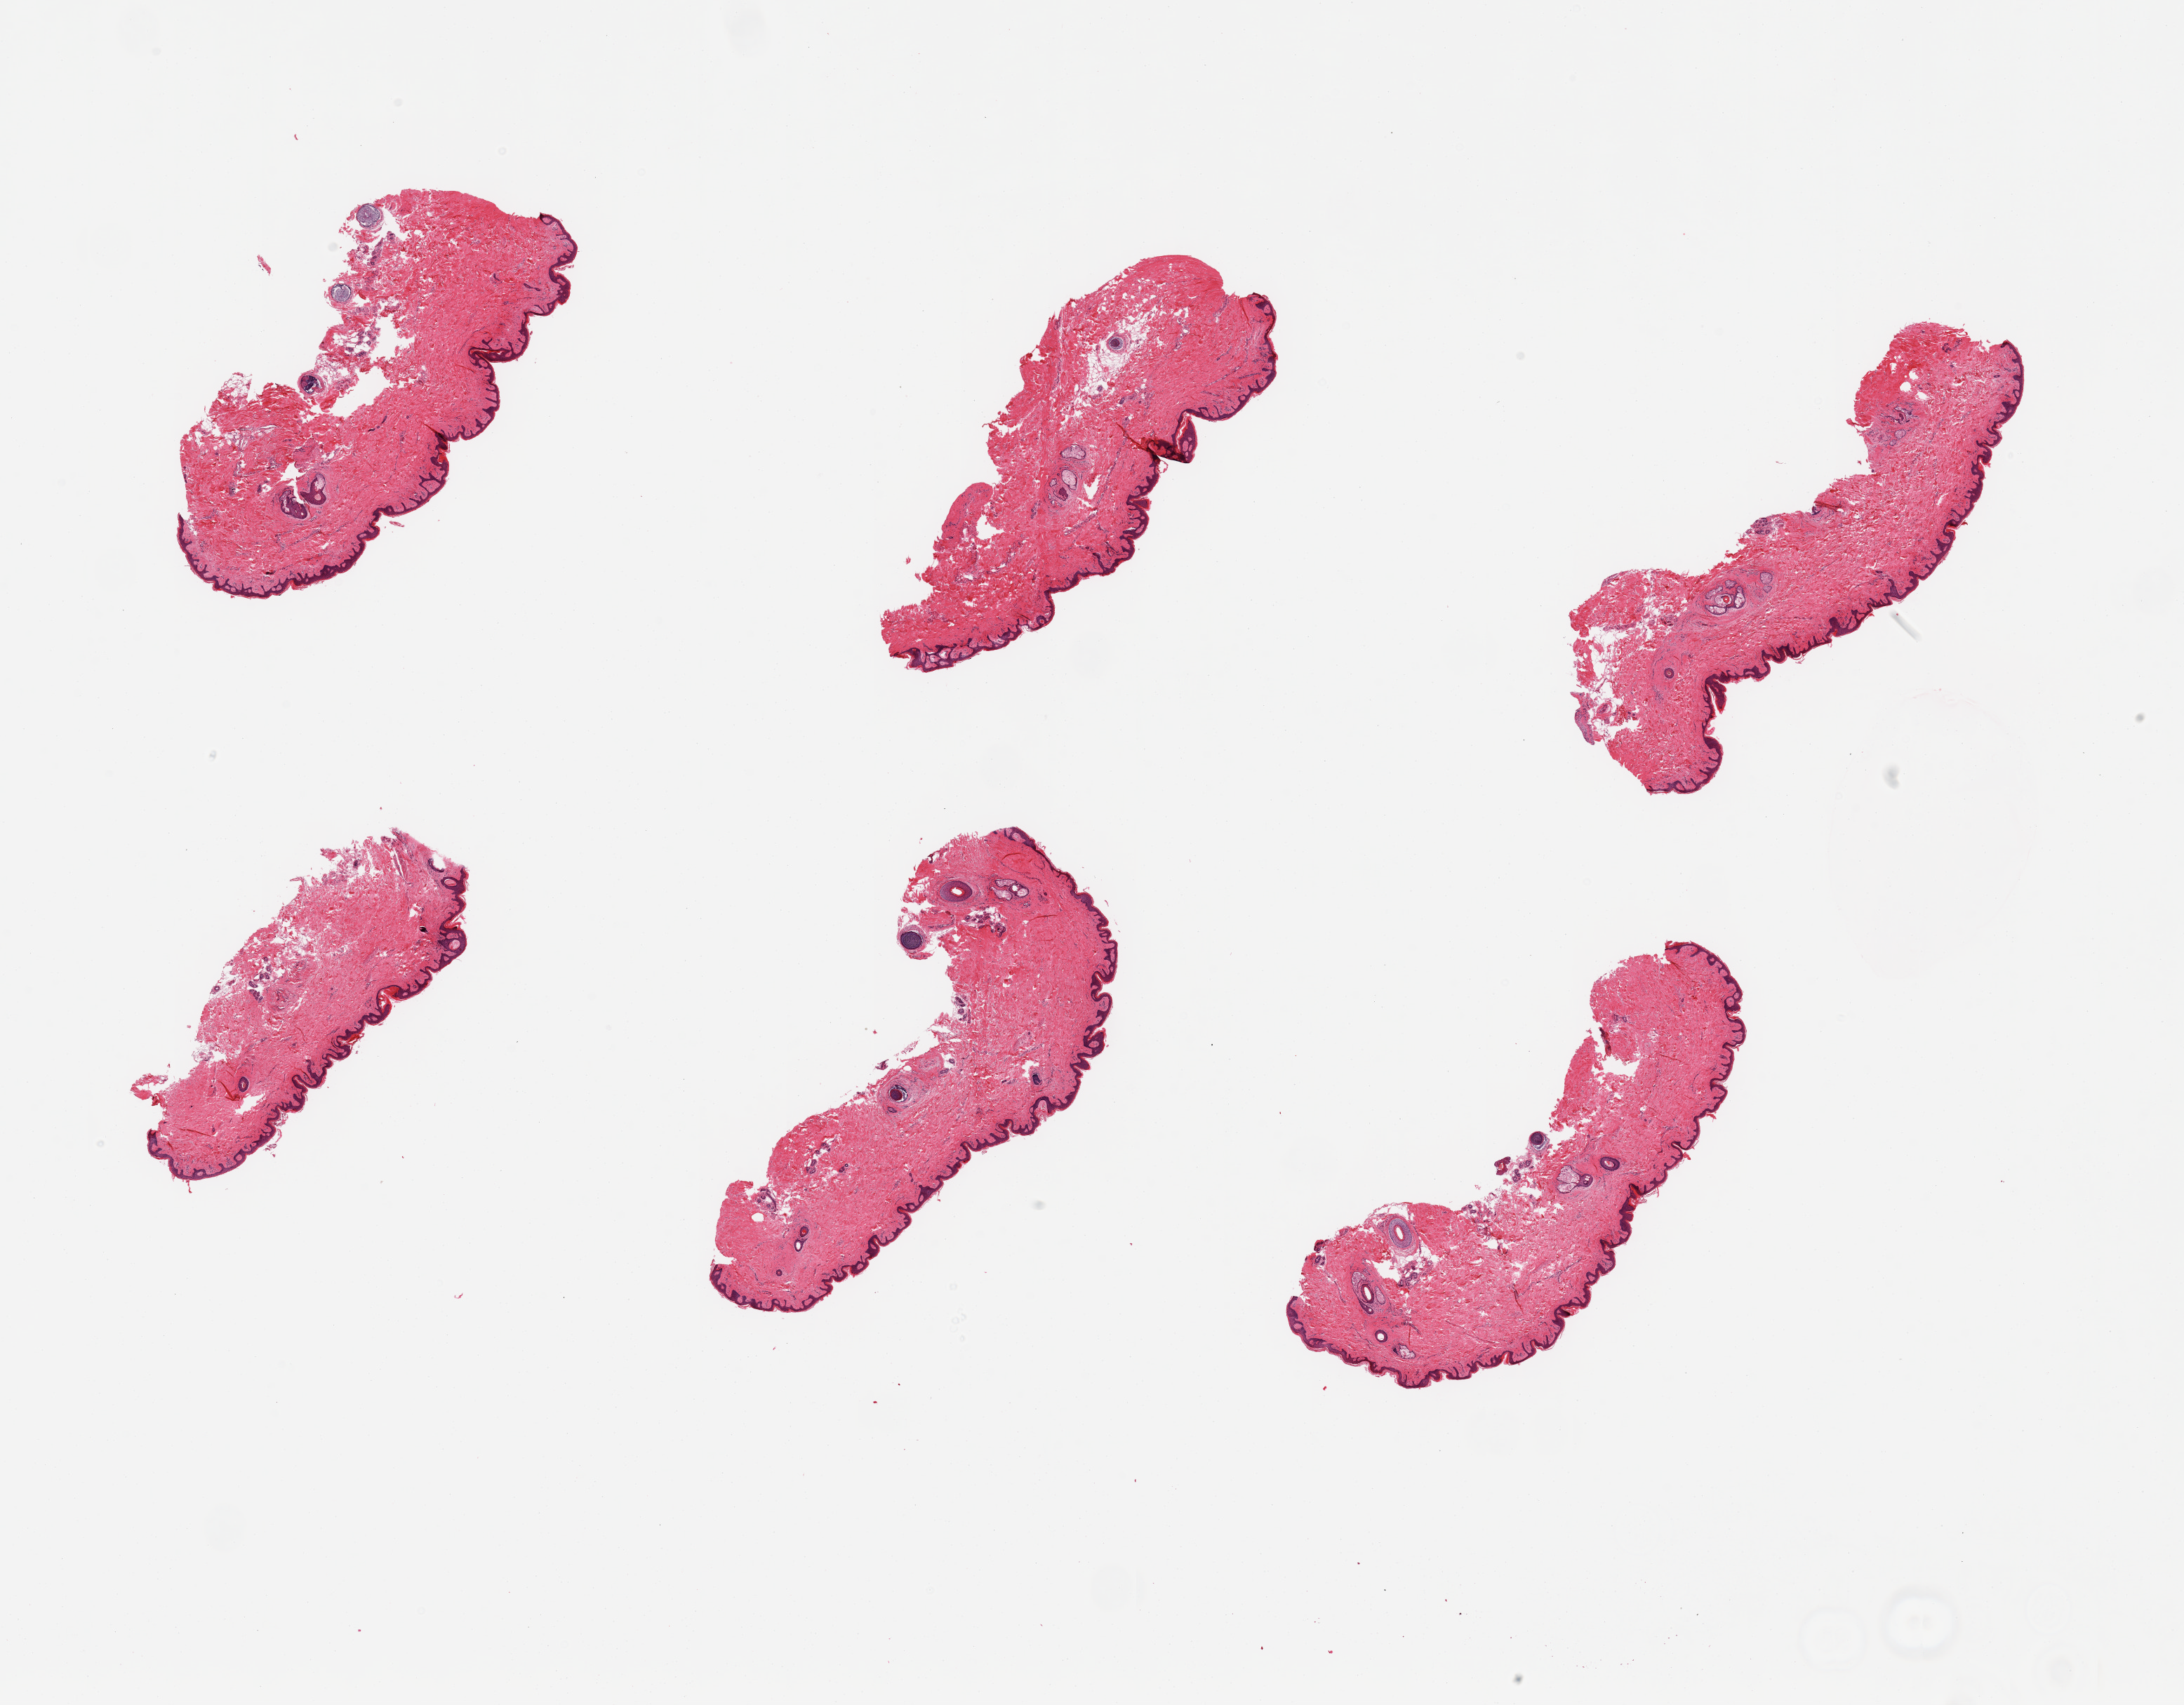
H&E whole-slide image — low-resolution overview of the scanned area, about 24.6 x 19.2 mm (acquisition: 20x scan); PAXgene-fixed, paraffin-embedded tissue; section of skin of suprapubic region (target tissue); tissue donor sample.
- review note (as recorded): 6 pieces; well trimmed; 5% dermal fat